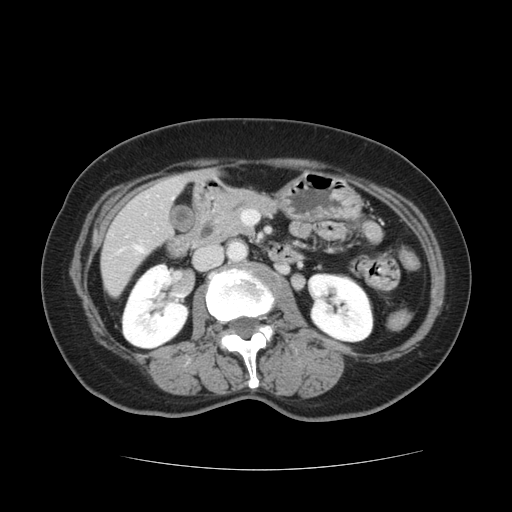
Contrast-enhanced abdominal CT, one axial slice. 120 kVp. Intravenous contrast given. Soft-tissue window (W 400 / L 40 HU). 2.5 mm slice thickness. 512 × 512 image matrix, field of view 366 × 366 mm. Female patient, age 67 years. Case-level facts recorded for this patient, not image findings: diagnosis: colorectal cancer liver metastases, imaged before liver resection; multiple liver metastases: yes; largest metastasis: 3 cm.
Structures marked on this image (outlined manually by an expert reader):
- hepatic veins: bounding box <135,246,143,252> (left, top, right, bottom; pixels)
- liver: <101,175,189,296>
- planned liver remnant (the part of the liver to remain after resection): <101,221,163,295>